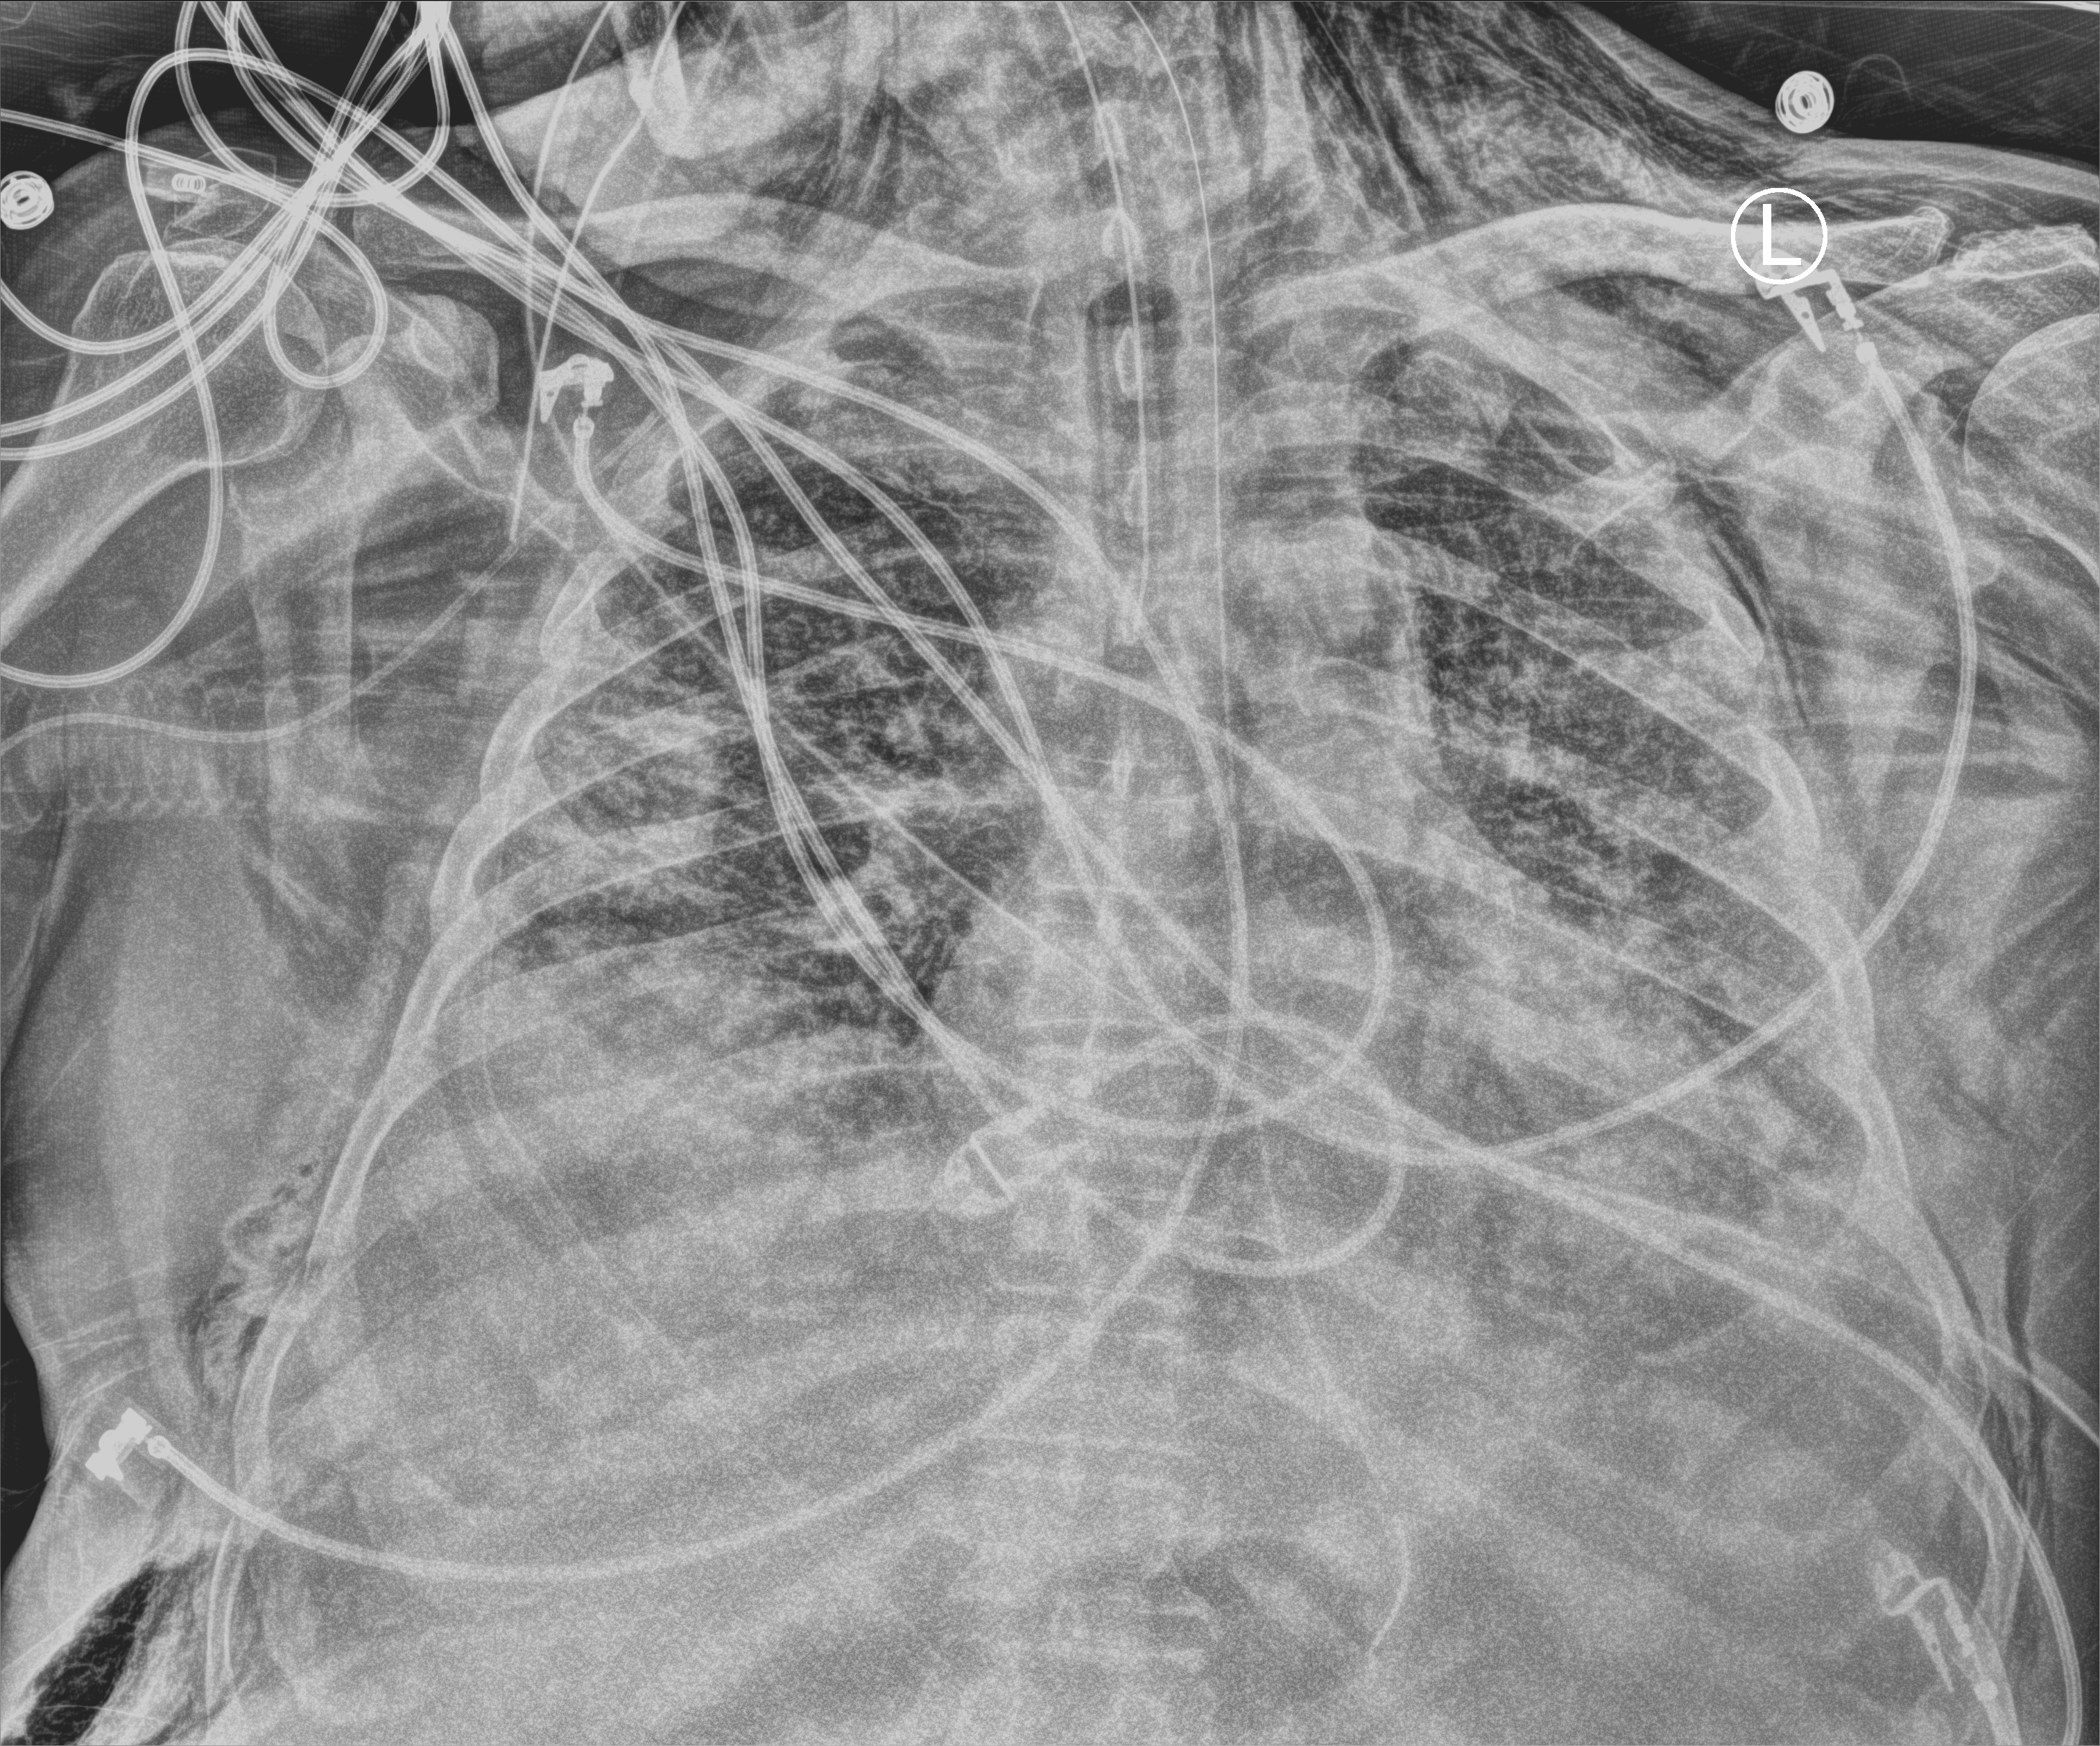
Bedside chest radiograph (computed radiography); anteroposterior (AP) projection. Male patient hospitalised with COVID-19, age 60–74 years.
Admission-level facts for this patient (not findings on this image; timing relative to this image not recorded): chronic kidney disease (admission record): no; mechanically ventilated during this hospital stay: yes; COPD (admission record): no.